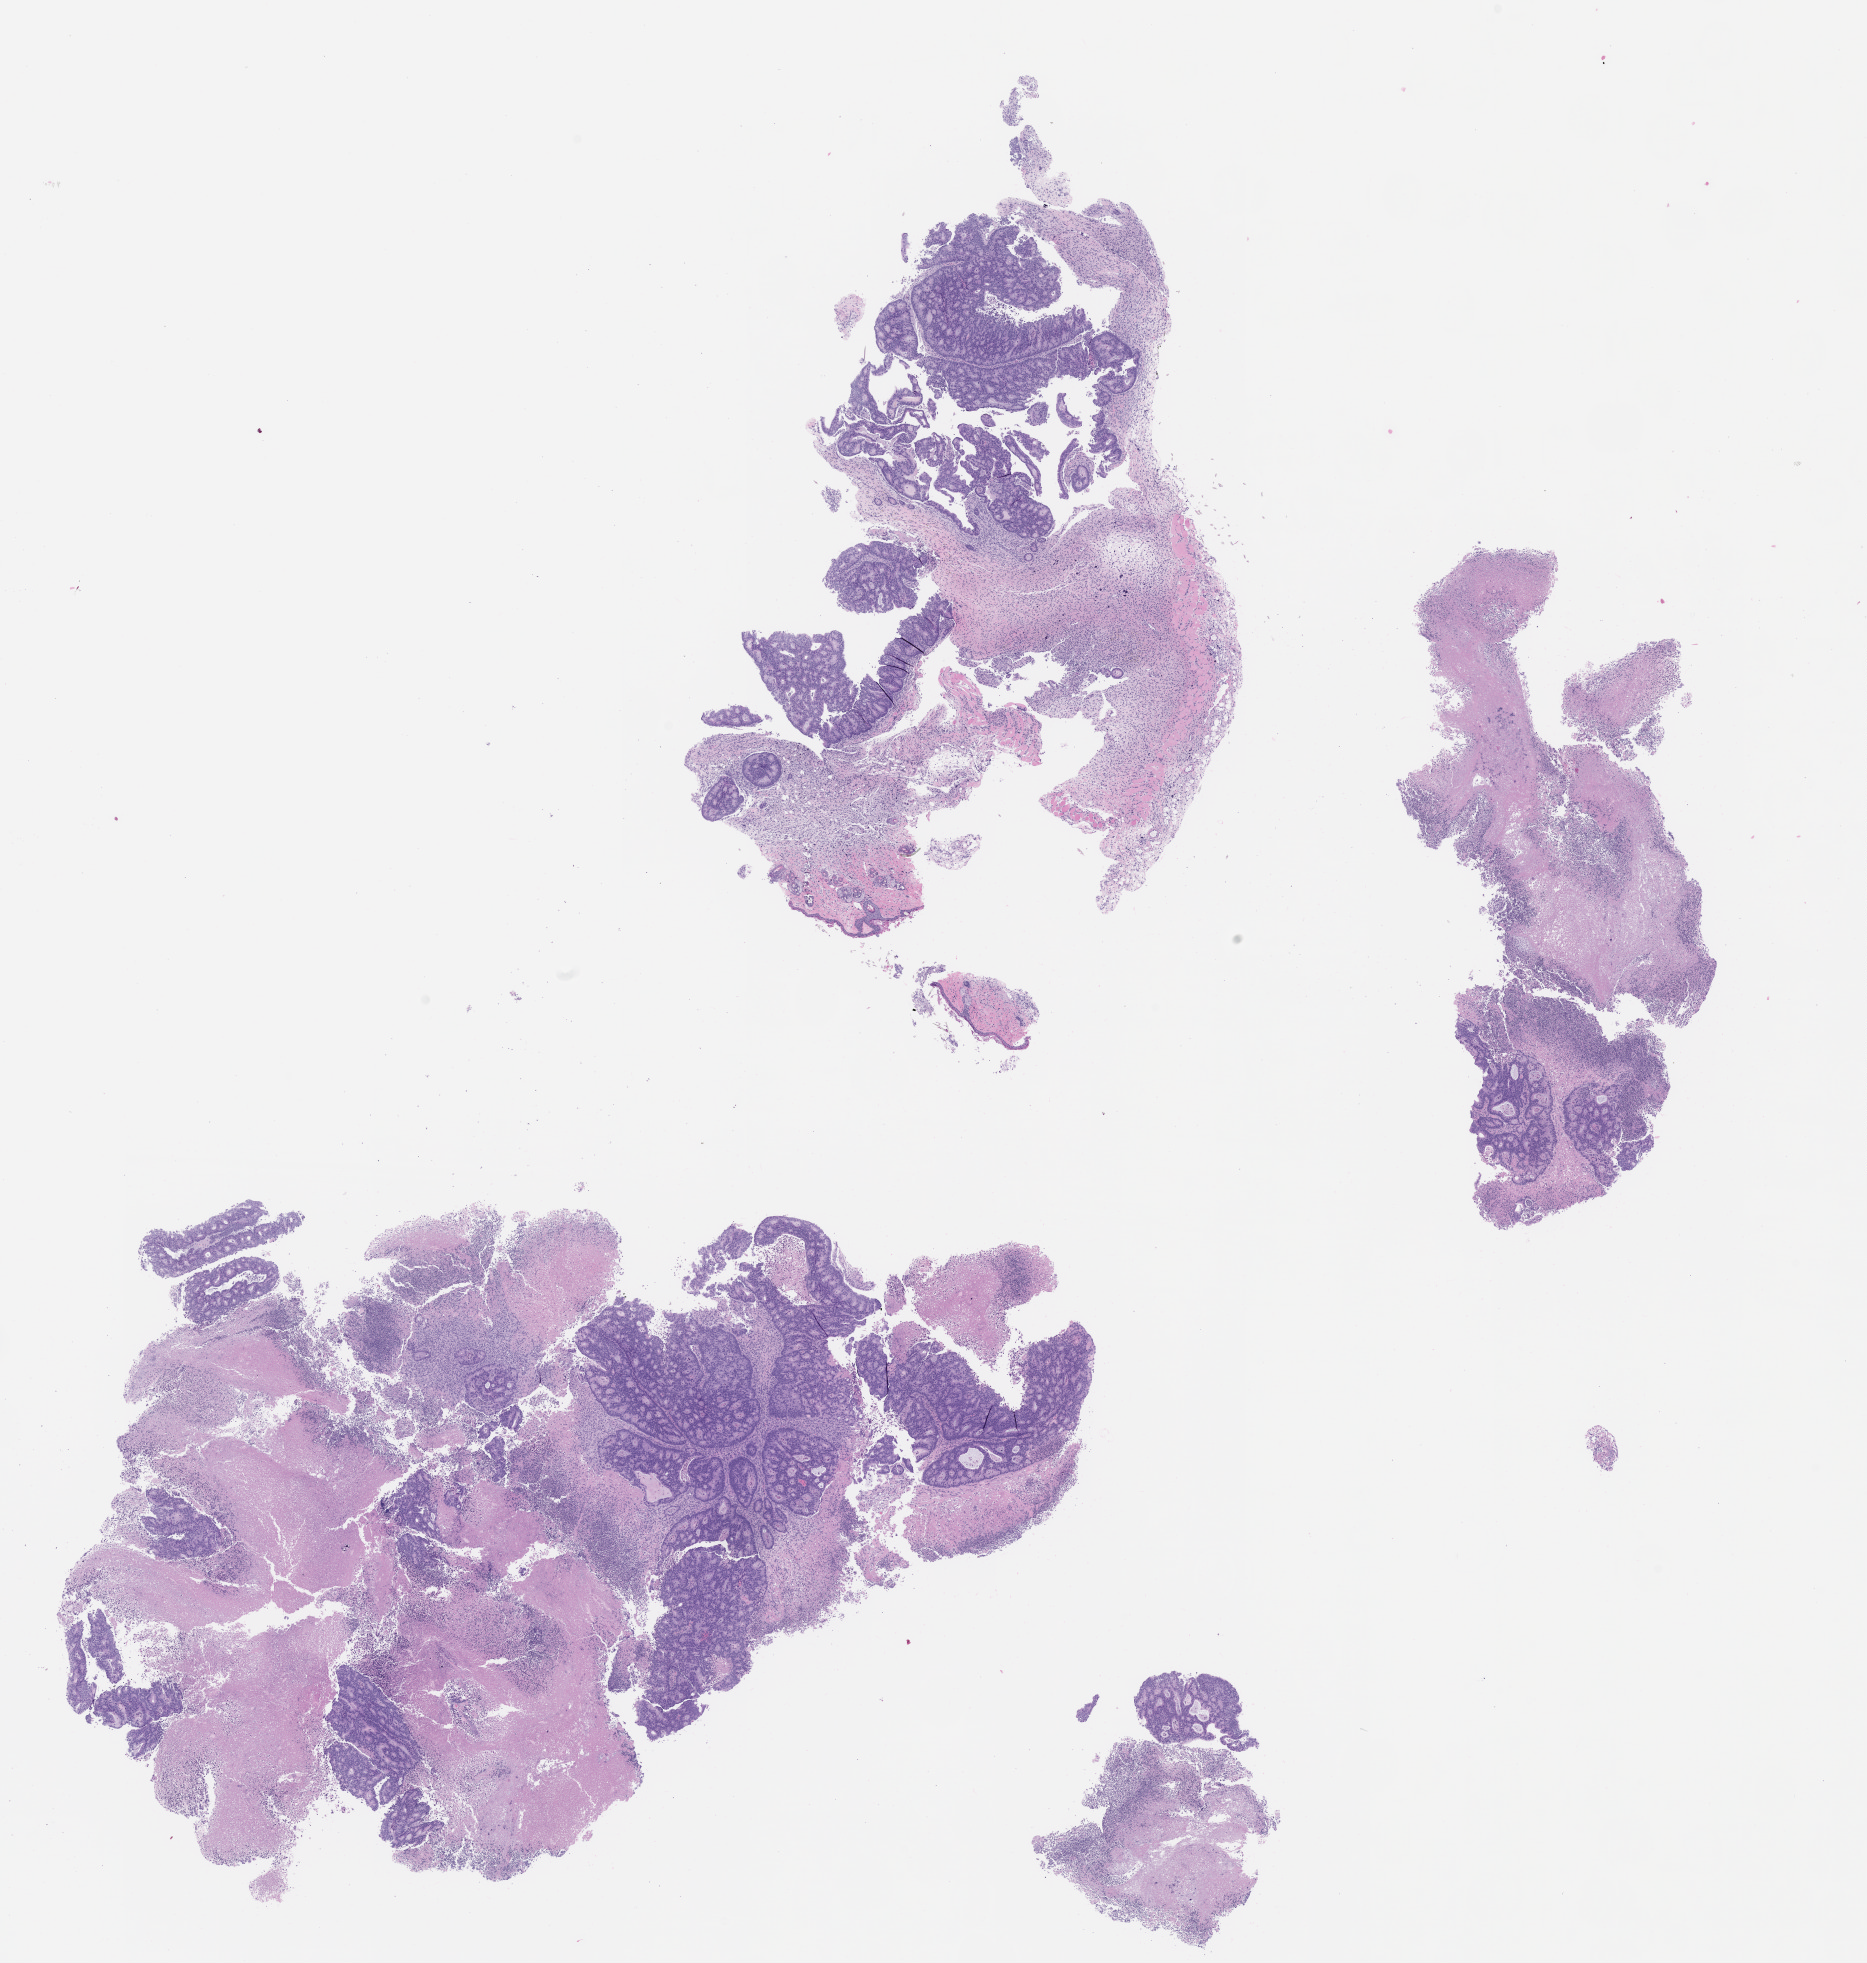
Whole-slide image, haematoxylin and eosin: patient-derived xenograft (human tumor grown in a mouse), passage 2 — low-resolution overview of the scanned area, about 15.0 x 15.8 mm. FFPE section. Originating tumor site category: colon.
* originating patient diagnosis: Colon Adenocarcinoma